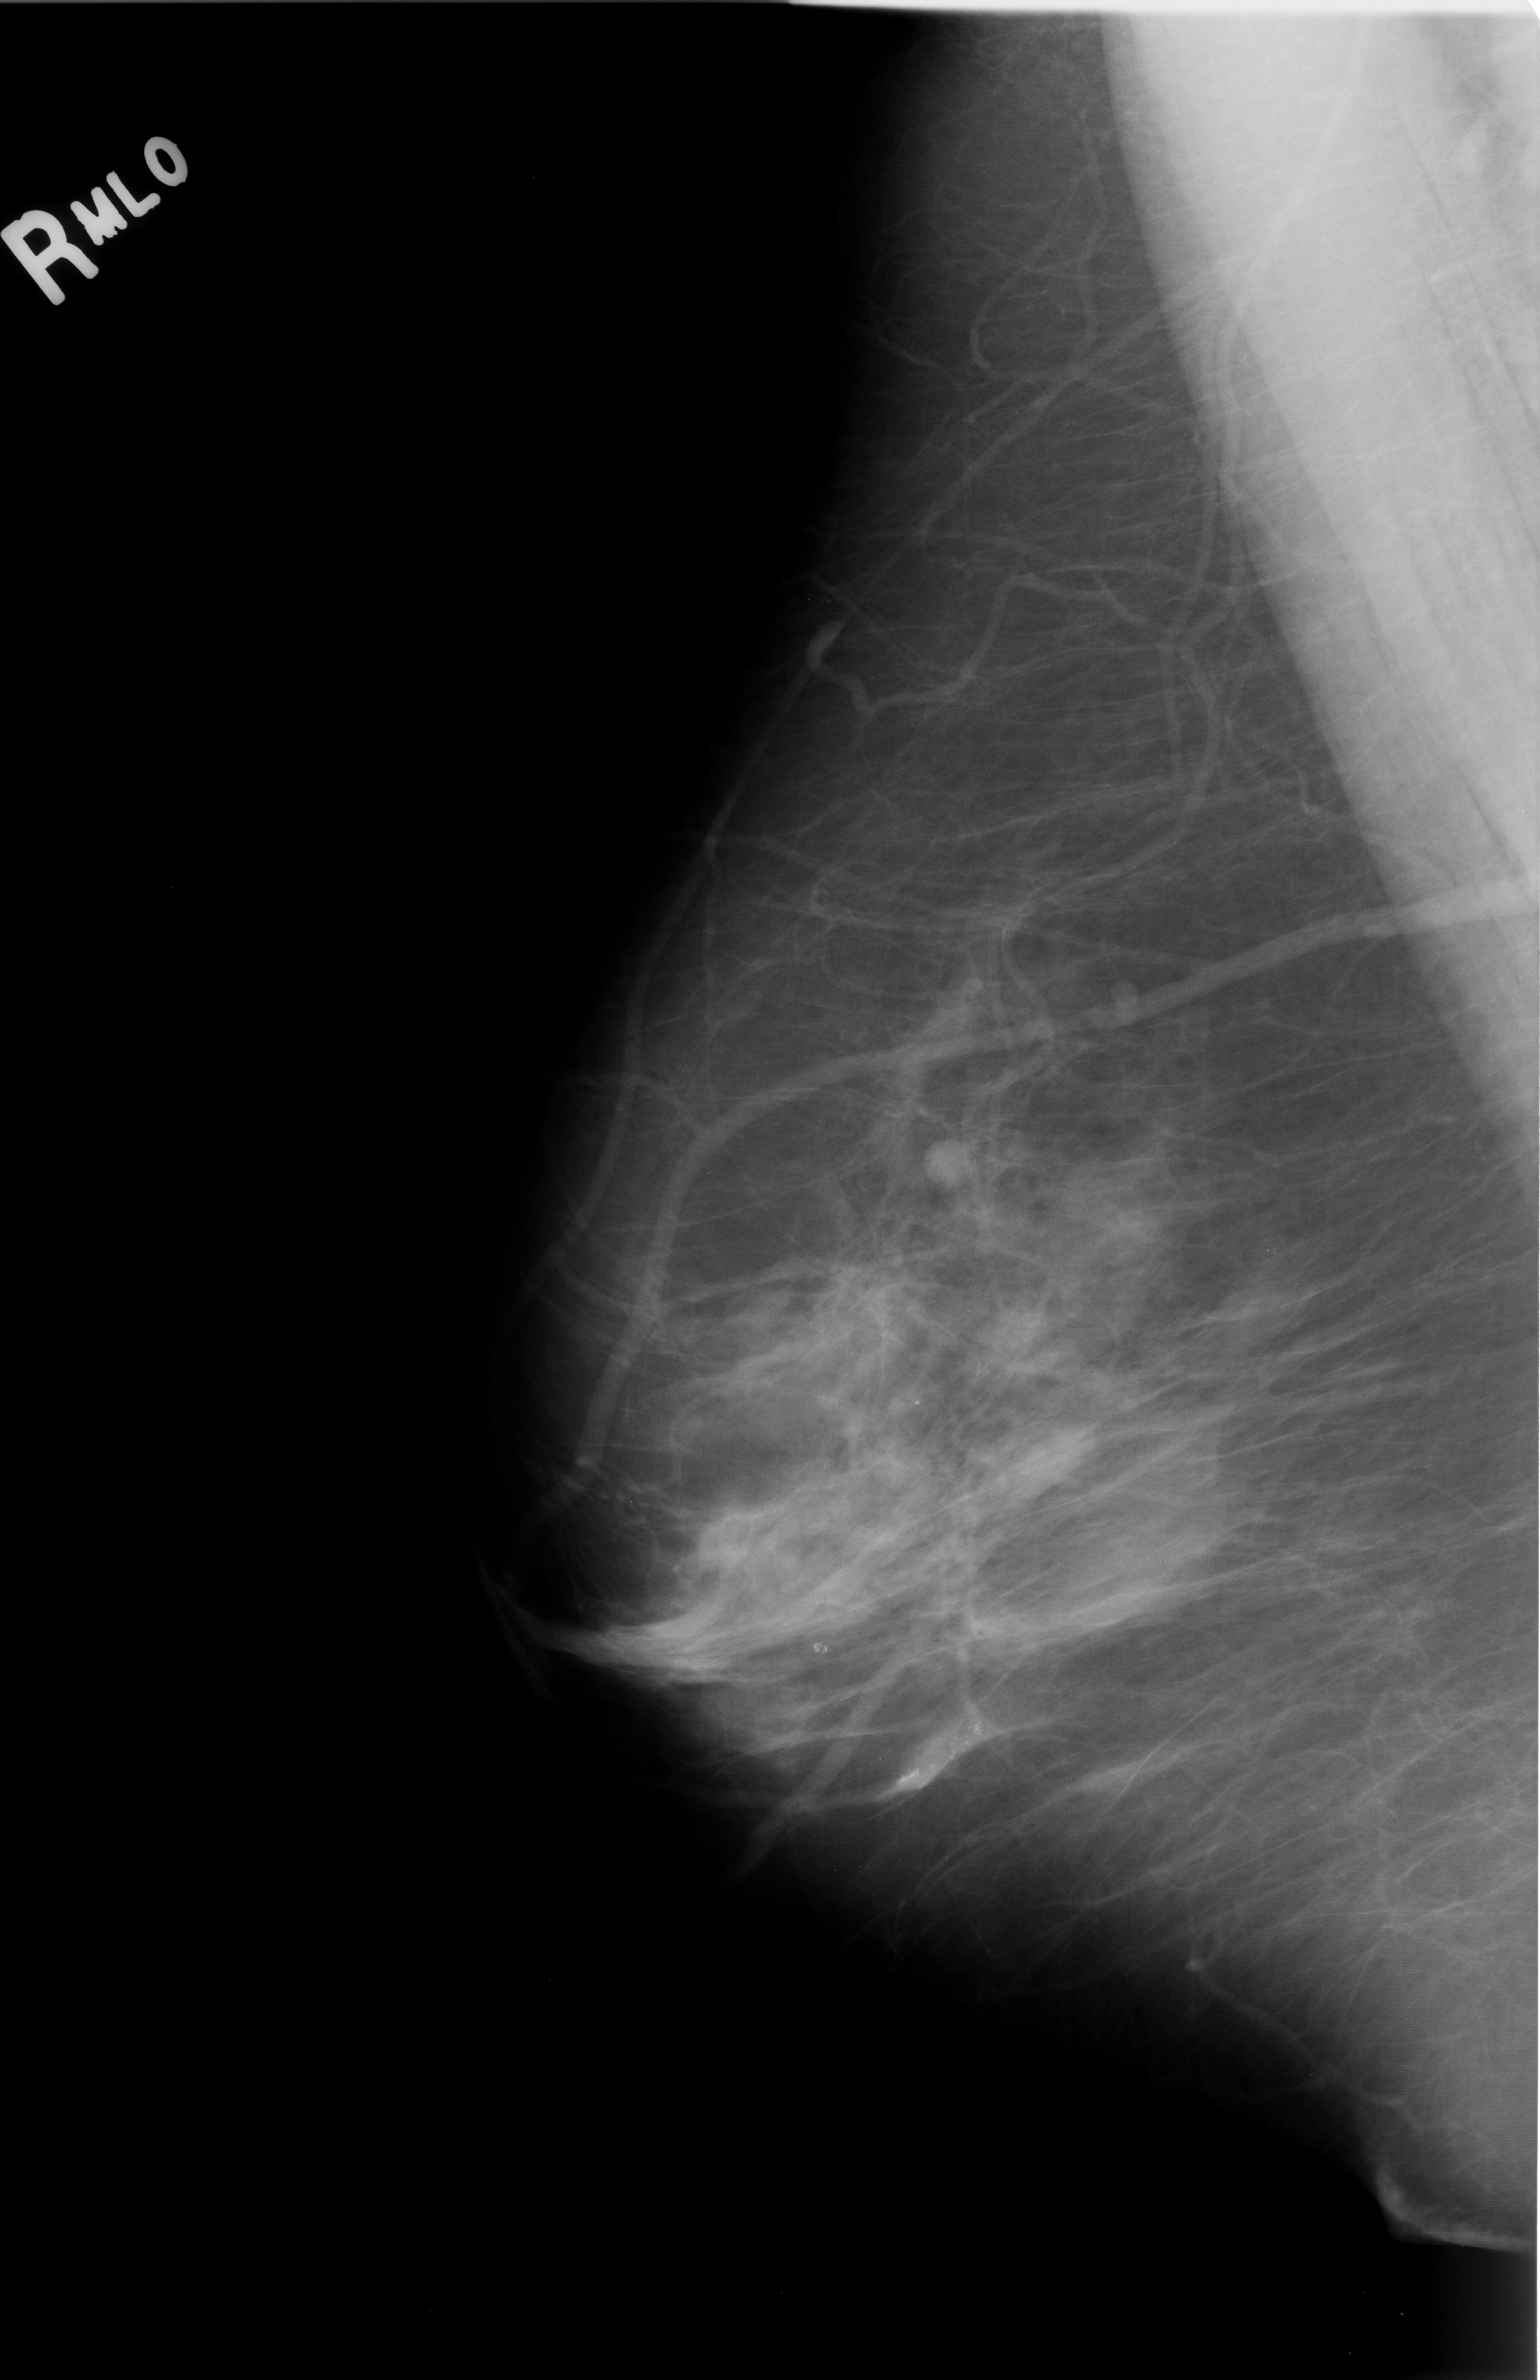
Digitized screen-film mammogram; right breast; MLO view; BI-RADS breast density category 2 (scale 1–4).
- Marked findings (only marked abnormalities are described; nothing is implied about the rest of the image): Finding 1 of 2: calcifications, morphology pleomorphic, distribution clustered; BI-RADS assessment category 3; pathology (as recorded): benign.
- Finding 2 of 2: calcifications, morphology pleomorphic, distribution clustered; BI-RADS assessment category 4; pathology (as recorded): benign.